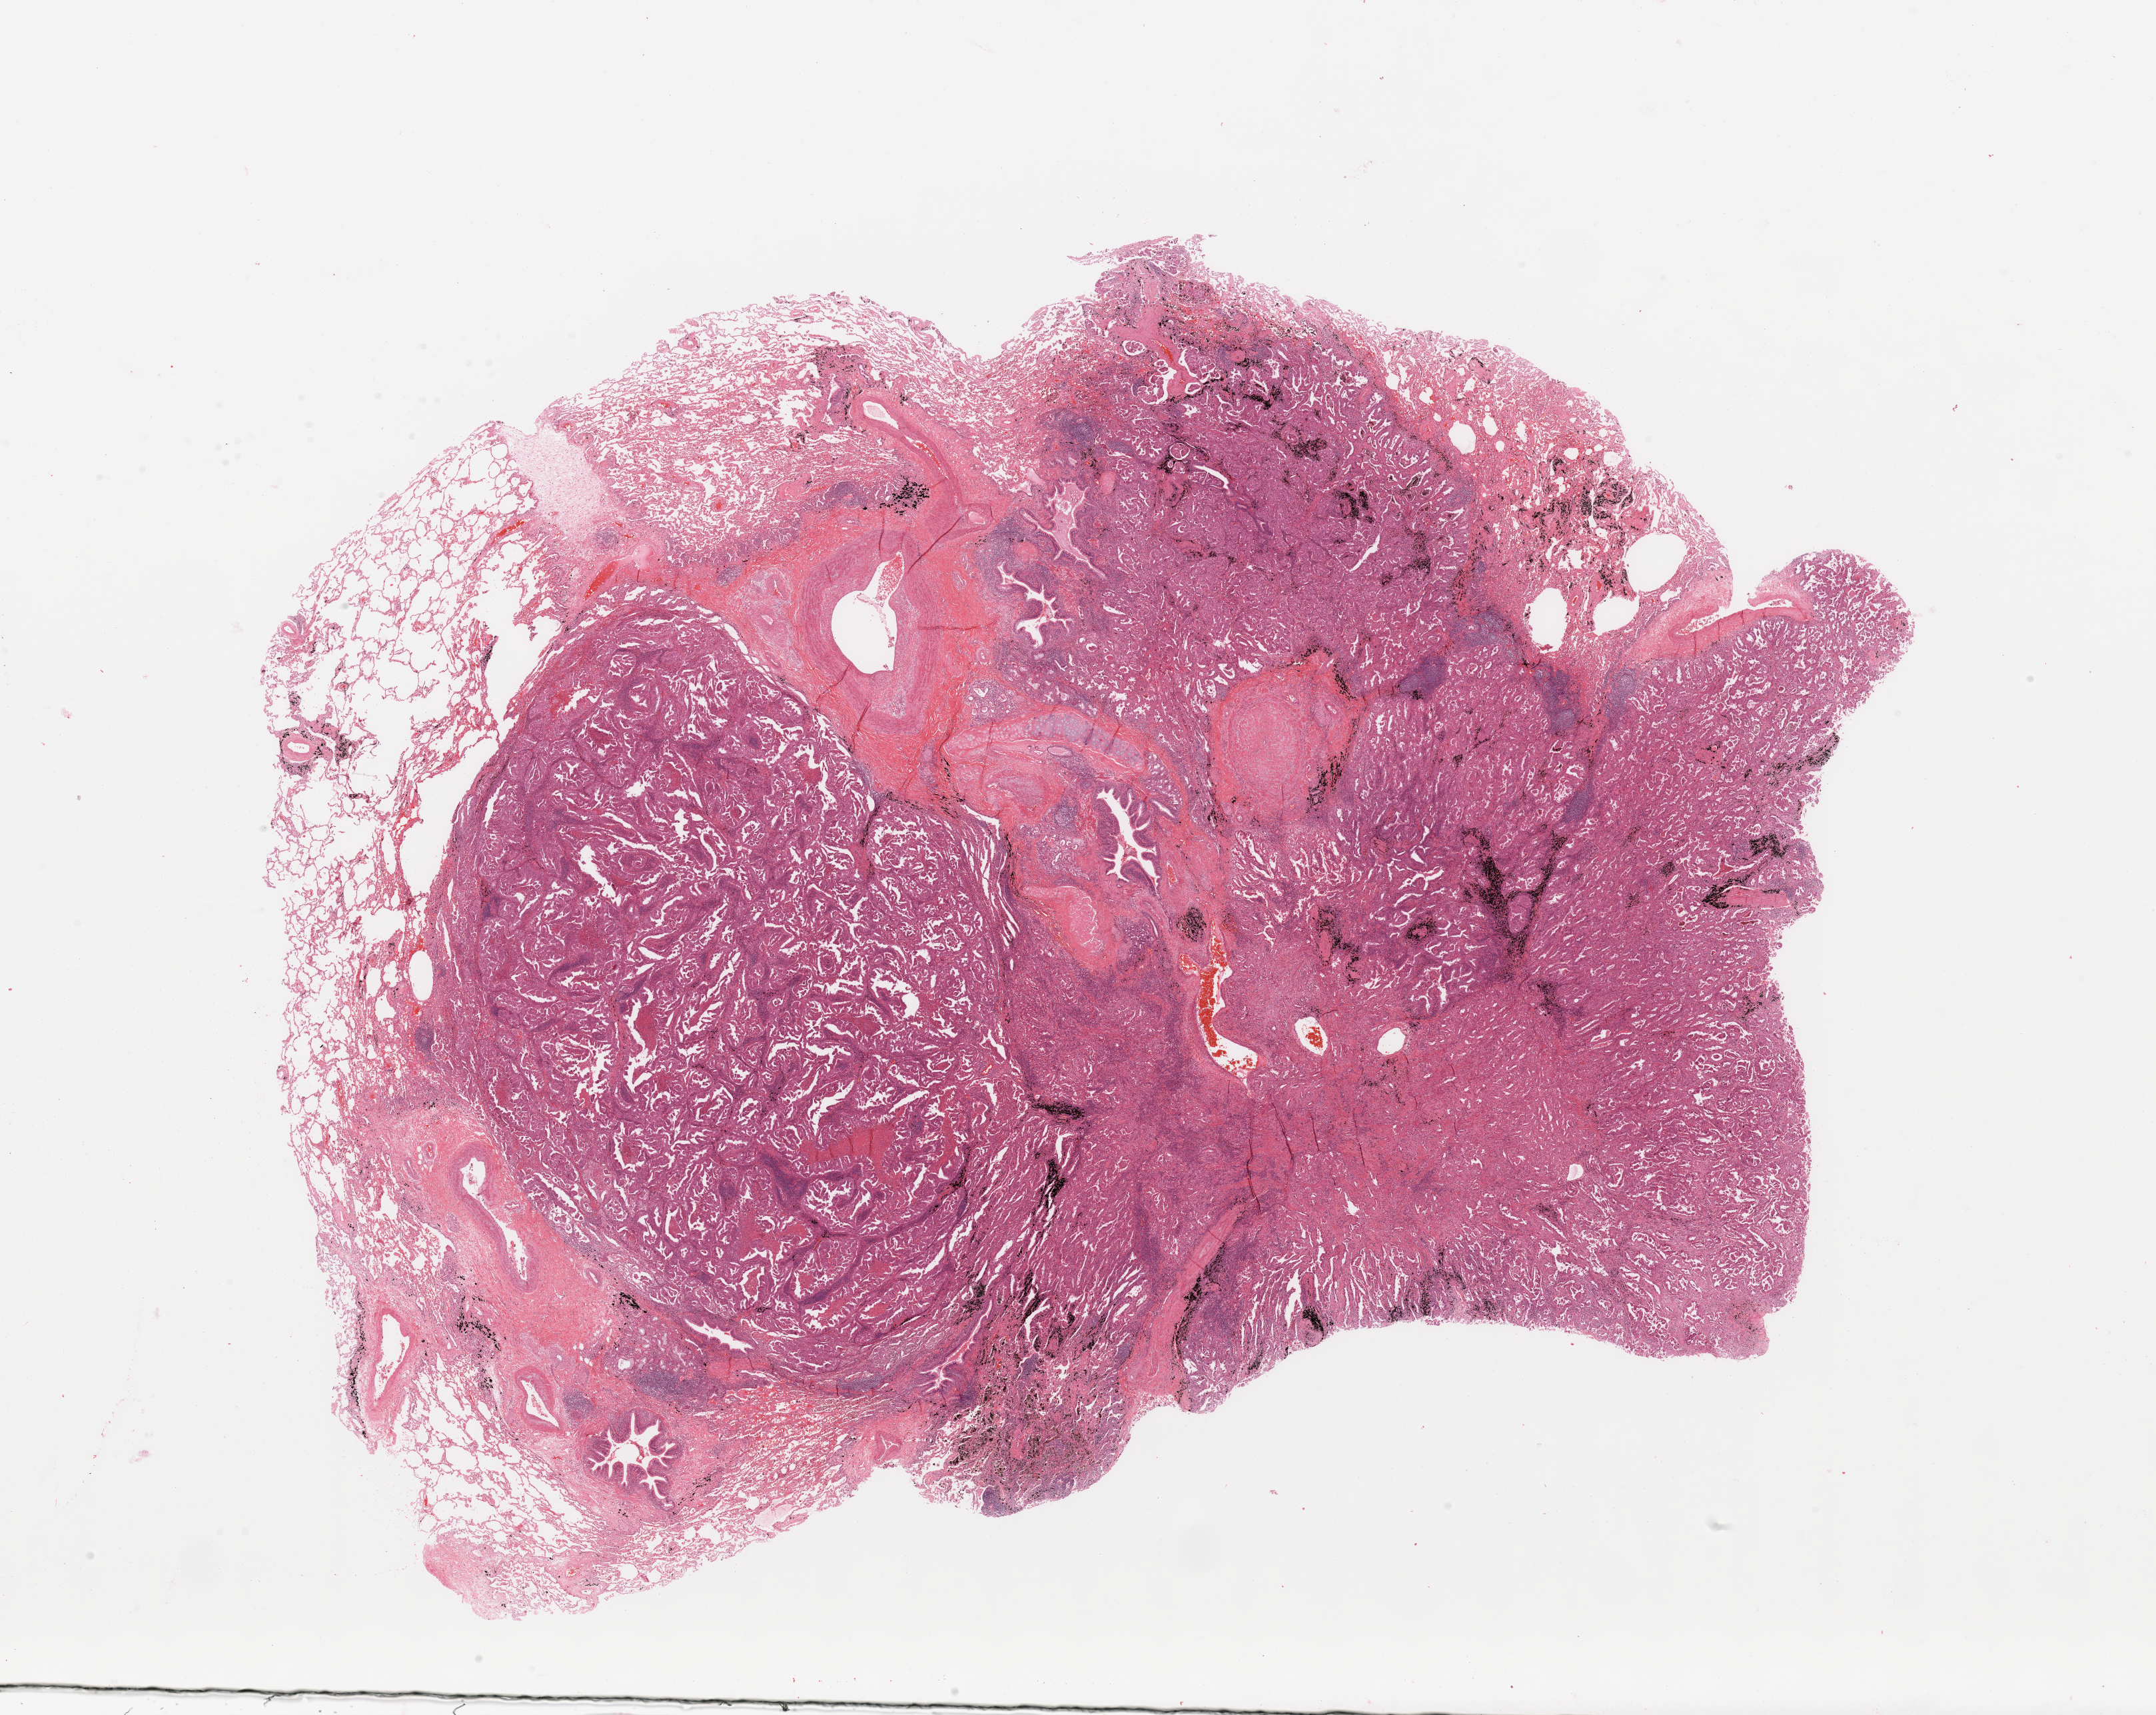
H&E-stained whole-slide image — whole scanned area (about 25.6 x 20.4 mm, acquisition: 20x scan) shown as a low-resolution overview, tumour tissue sample, sampled site: lung. 72-year-old male patient. Histologic grade: G2 (moderately differentiated). Slide review estimates, as recorded: tumour nuclei 65%, necrosis 5%.
Diagnosis: Adenocarcinoma, NOS. AJCC pathologic stage: IB.